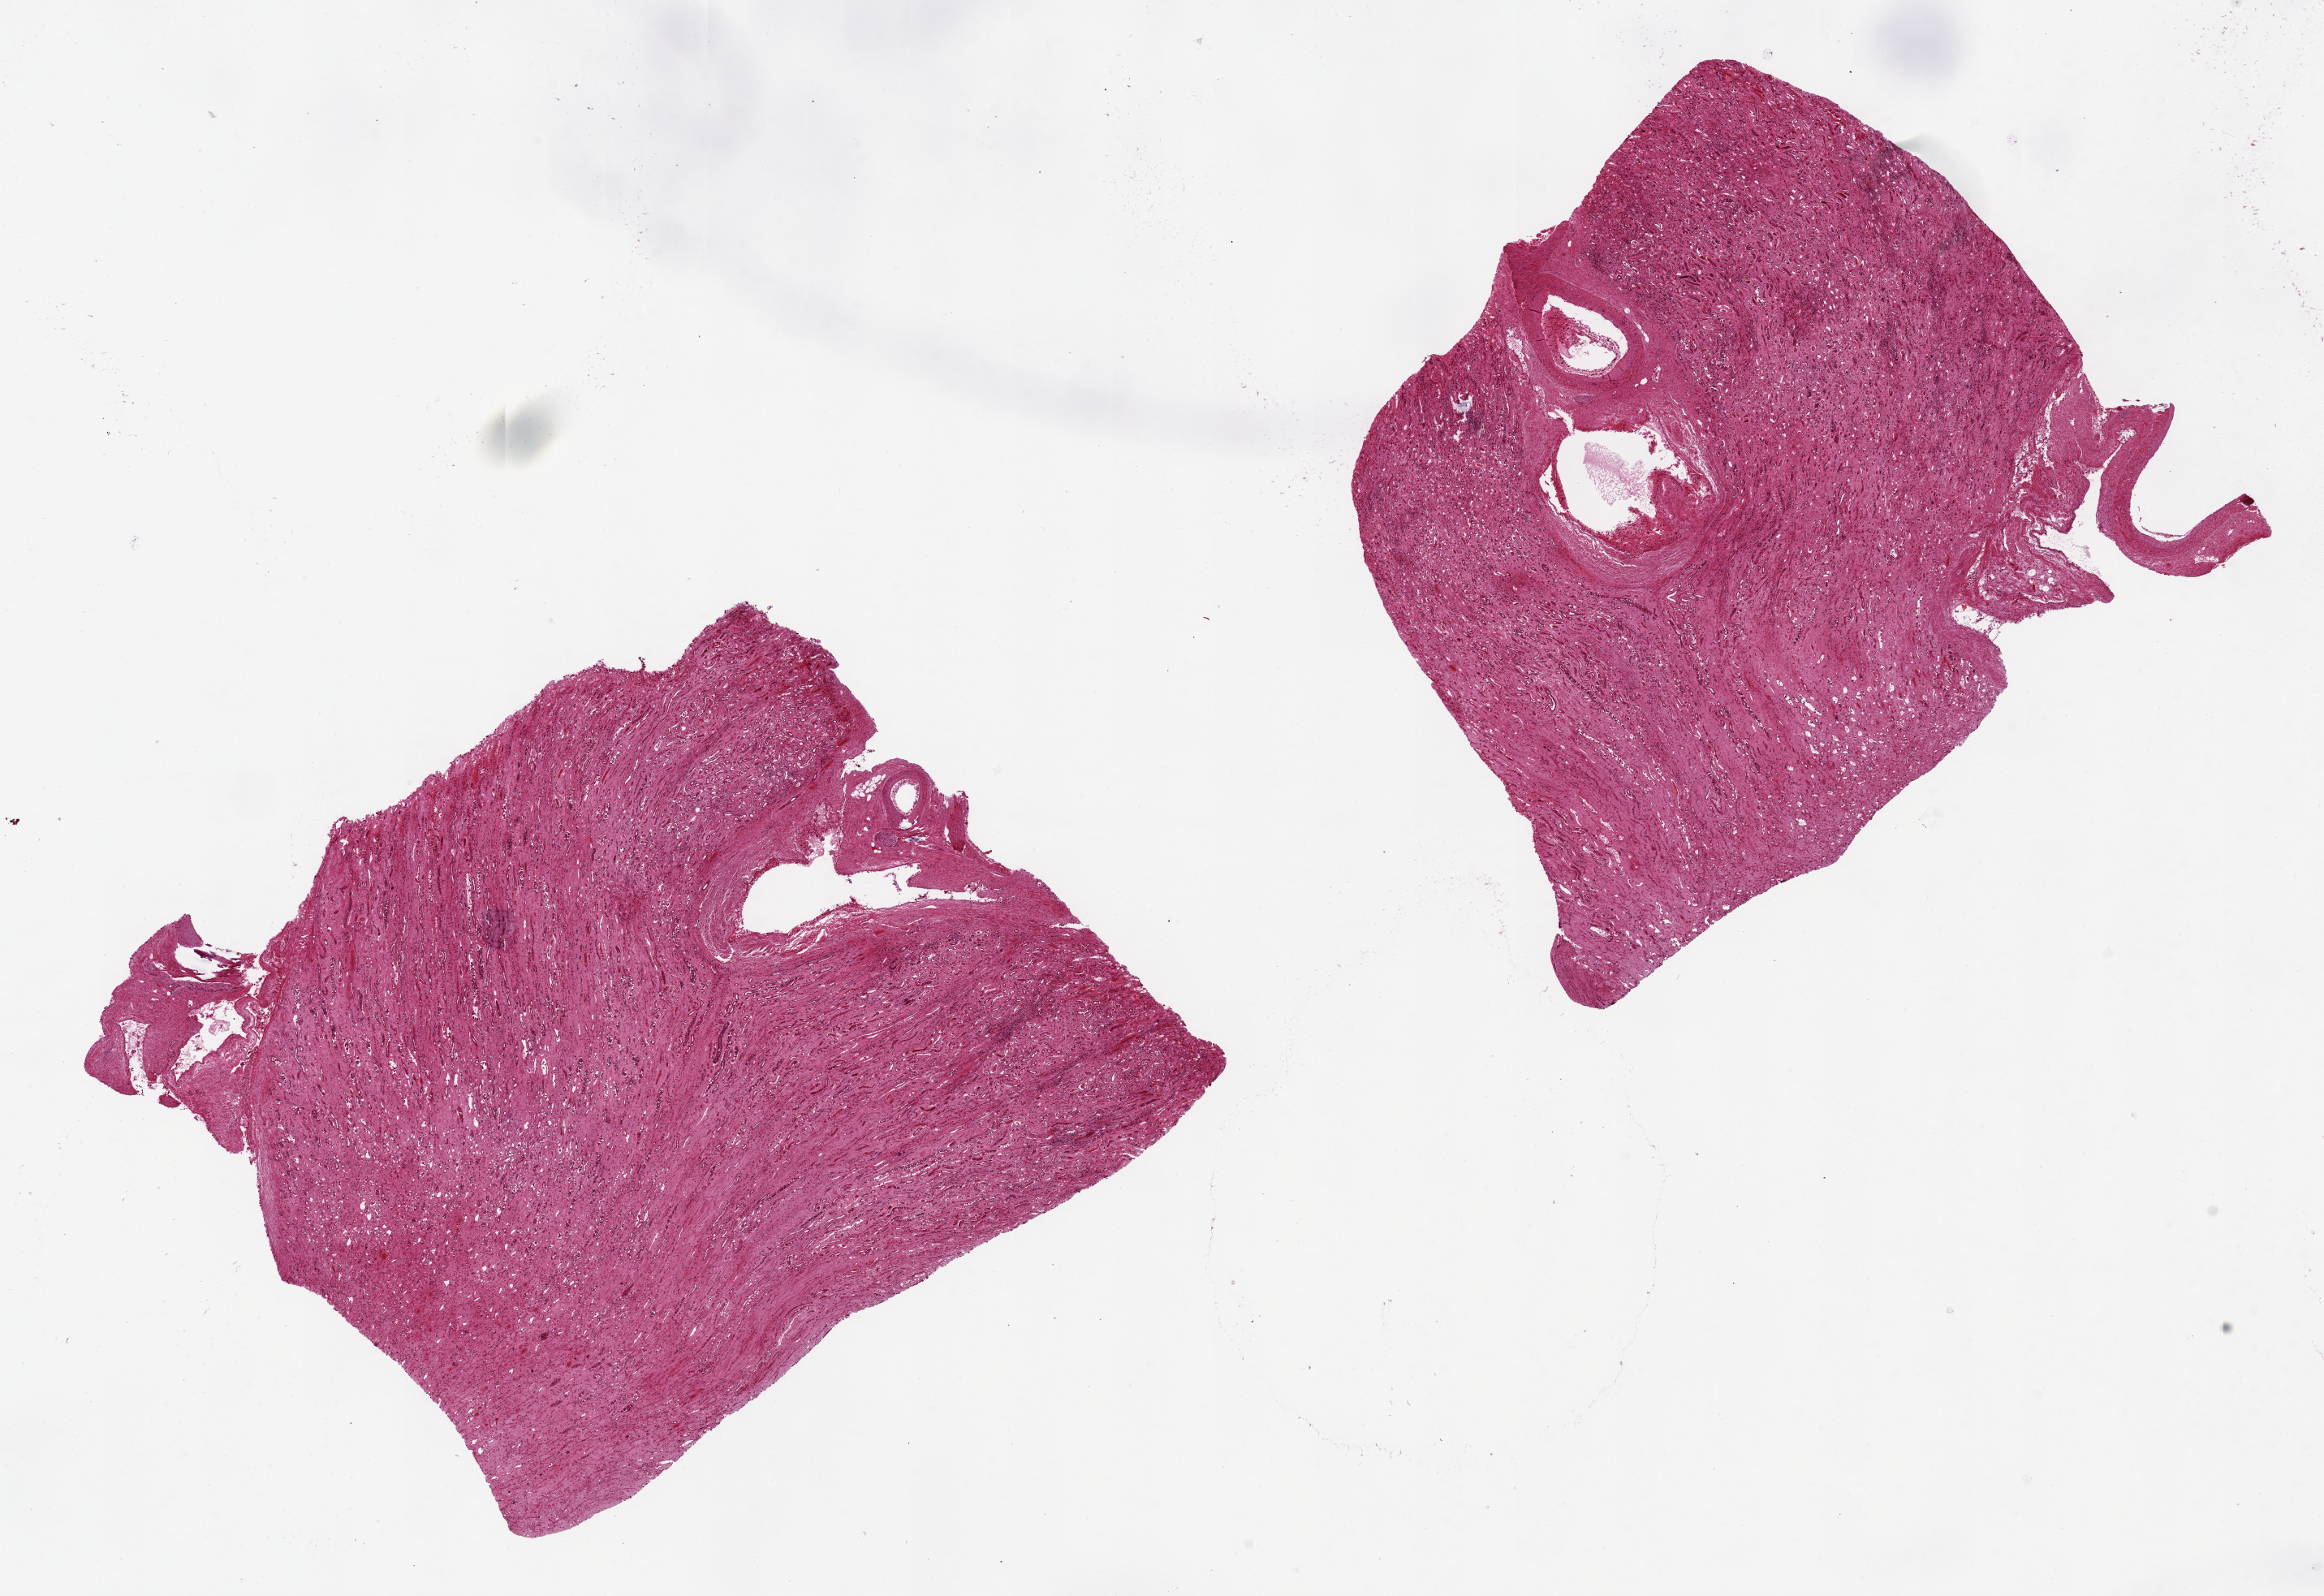
Hematoxylin and eosin (H&E) whole-slide image, shown as a low-resolution overview of the whole scanned area (about 22.6 x 15.5 mm, from a 20x scan). PAXgene-fixed paraffin-embedded (PFPE) section. Section of renal medulla (target tissue). Donor tissue sample. Donor sex: female.
* pathologist's review note for this sample: 2 pieces 8x7 & 7x6 mm; all medulla, no cortex